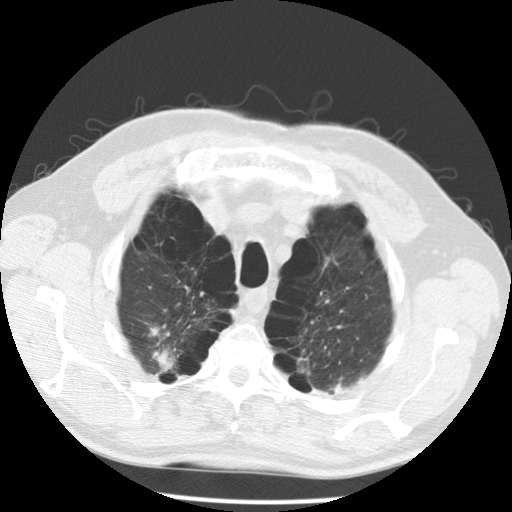
Axial slice from a low-dose chest CT screening exam; second screening round (one year after baseline); lung window (W 1500 / L -600 HU); 2.5 mm slice thickness; 512 × 512 image matrix. Male participant, aged 68 years at enrolment. Former smoker at enrolment.
Expert reader's lesion annotation, bounding box <124,309,198,385> (left, top, right, bottom; pixels). The screening reader recorded 2 non-calcified nodules or masses ≥4 mm on this exam; which of them this box marks is not recorded. Later outcome: lung cancer diagnosed 617 days after this screen — large cell carcinoma, NOS, right upper lobe, poorly differentiated (G3), stage IV (AJCC 6th edition).